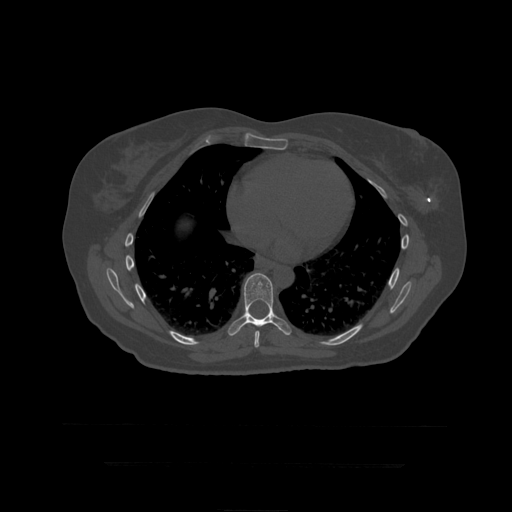
CT including the spine, one axial slice; position 265 of 399 along the scan axis; 120 kVp; bone window (W 1800 / L 400 HU); 1.25 mm slice thickness; 512 × 512 image matrix, field of view 450 × 450 mm. Patient age 41 years. From the clinical record (not read from this slice): primary cancer: breast.
Outlined on this slice (semi-automatically segmented with operator editing):
- T8 vertebra: box from (x=254, y=331) to (x=260, y=348) px
- T9 vertebra: (x=228, y=273)–(x=292, y=336)